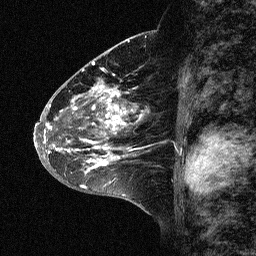
Breast MRI (dynamic contrast-enhanced), one sagittal slice. Position 32 of 64 along the scan axis. Dynamic contrast-enhanced study with each time point stored as its own series, time point 2 of 3 at this slice position (early post-contrast, ordered by acquisition time). 1.5 T. TE 4.5 ms, TR 11 ms. 2.06 mm slice thickness. 256 × 256 image matrix, field of view 200 × 200 mm. Patient: female, 46 years. Case-level facts recorded for this patient, not image findings: setting: breast cancer imaged before/during neoadjuvant chemotherapy; receptor status: HER2-positive.
Outlined on this slice (semi-automatically segmented with operator editing):
- analysis volume of interest (the breast-tissue region the enhancement analysis was run in; not a lesion): bounding box (x1, y1, x2, y2) in pixels: (43, 72, 168, 177)
- tumour enhancement mask (voxels above the 90 % enhancement threshold inside the analysis volume of interest): (44, 74, 166, 173)